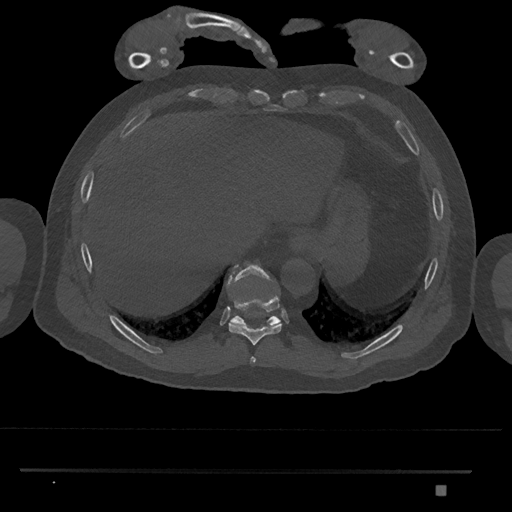
CT including the spine, one axial slice; slice 1039 of 1134 in the series (ordered by position); 120 kVp; bone window (W 1800 / L 400 HU); 0.5 mm slice thickness; 512 × 512 image matrix, field of view 429 × 429 mm. Patient: male, 65 years. From the clinical record (not read from this slice): primary cancer: prostate.
Outlined on this slice (semi-automatic segmentation, software-assisted and operator-edited):
- T10 vertebra: box from (x=227, y=264) to (x=281, y=327) px
- T8 vertebra: (x=250, y=357)–(x=256, y=364)
- T9 vertebra: (x=228, y=296)–(x=282, y=346)